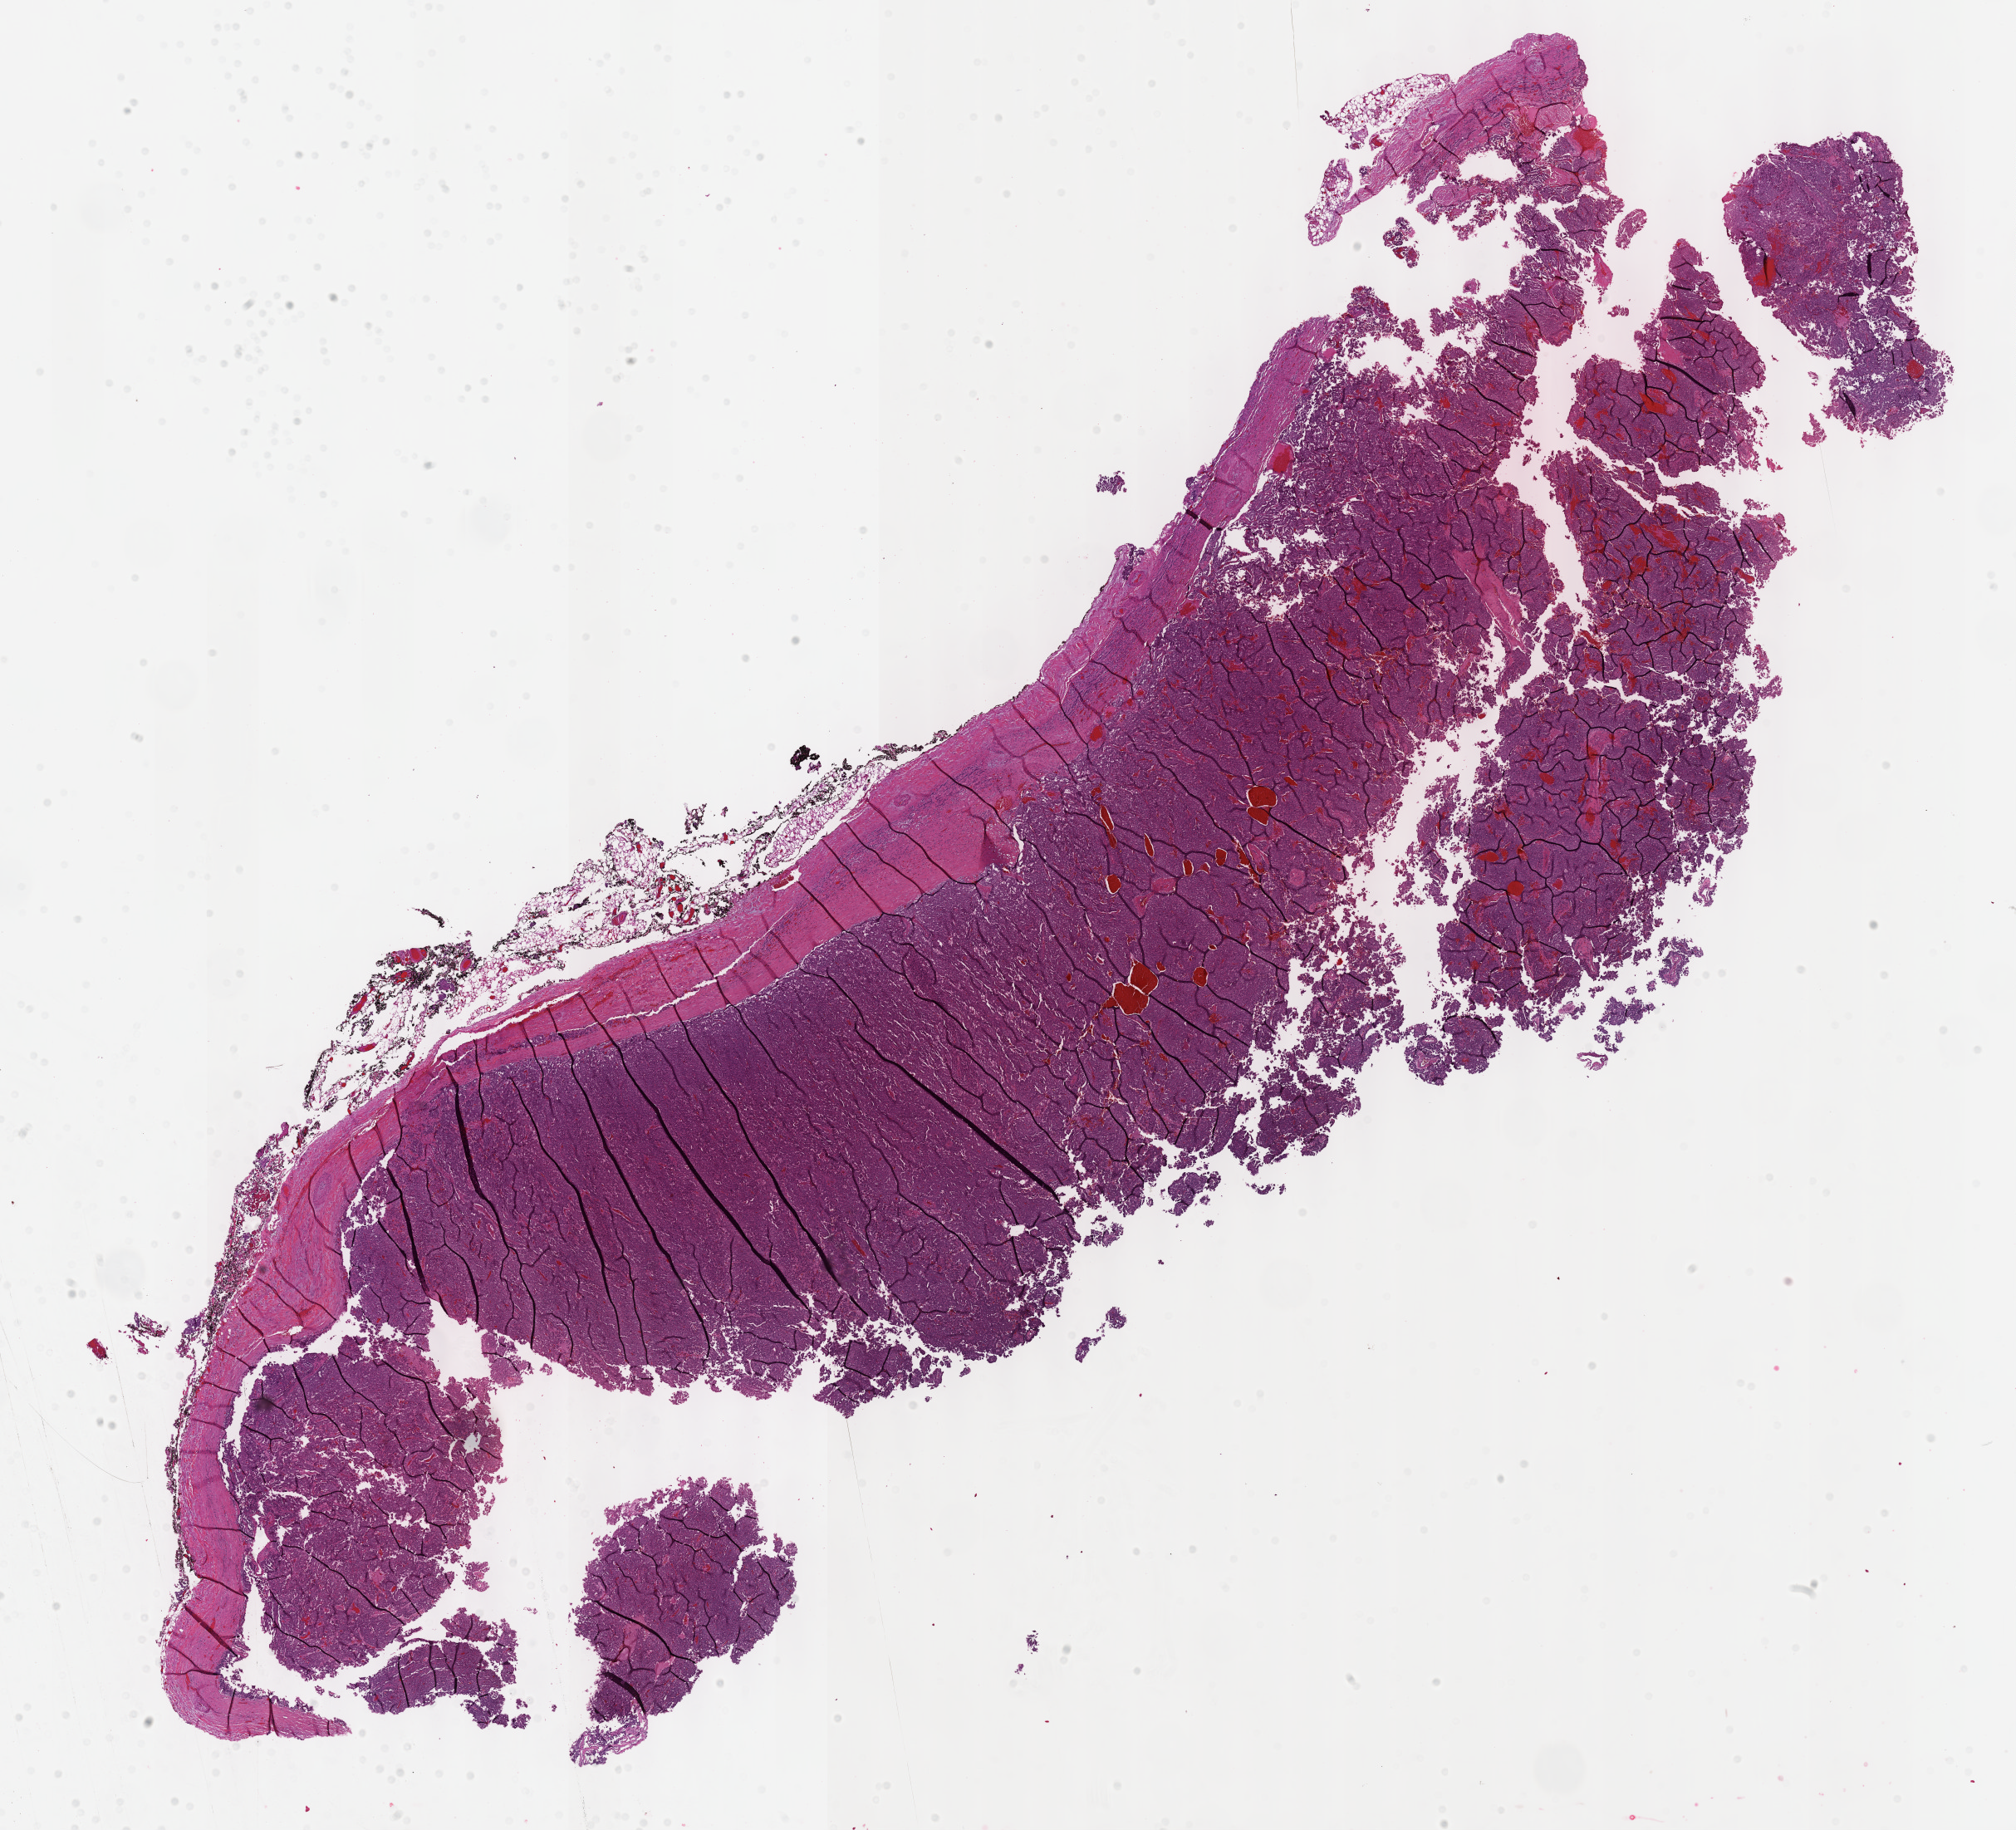
Whole-slide histology image, H&E-stained, low-resolution overview of the scanned area, about 19.6 x 17.8 mm (slide scanned at 40x); FFPE section; primary tumour sample from the adrenal gland. Patient: female, age at initial diagnosis 30 years.
Laterality: right. Histologic diagnosis: Pheochromocytoma, NOS.